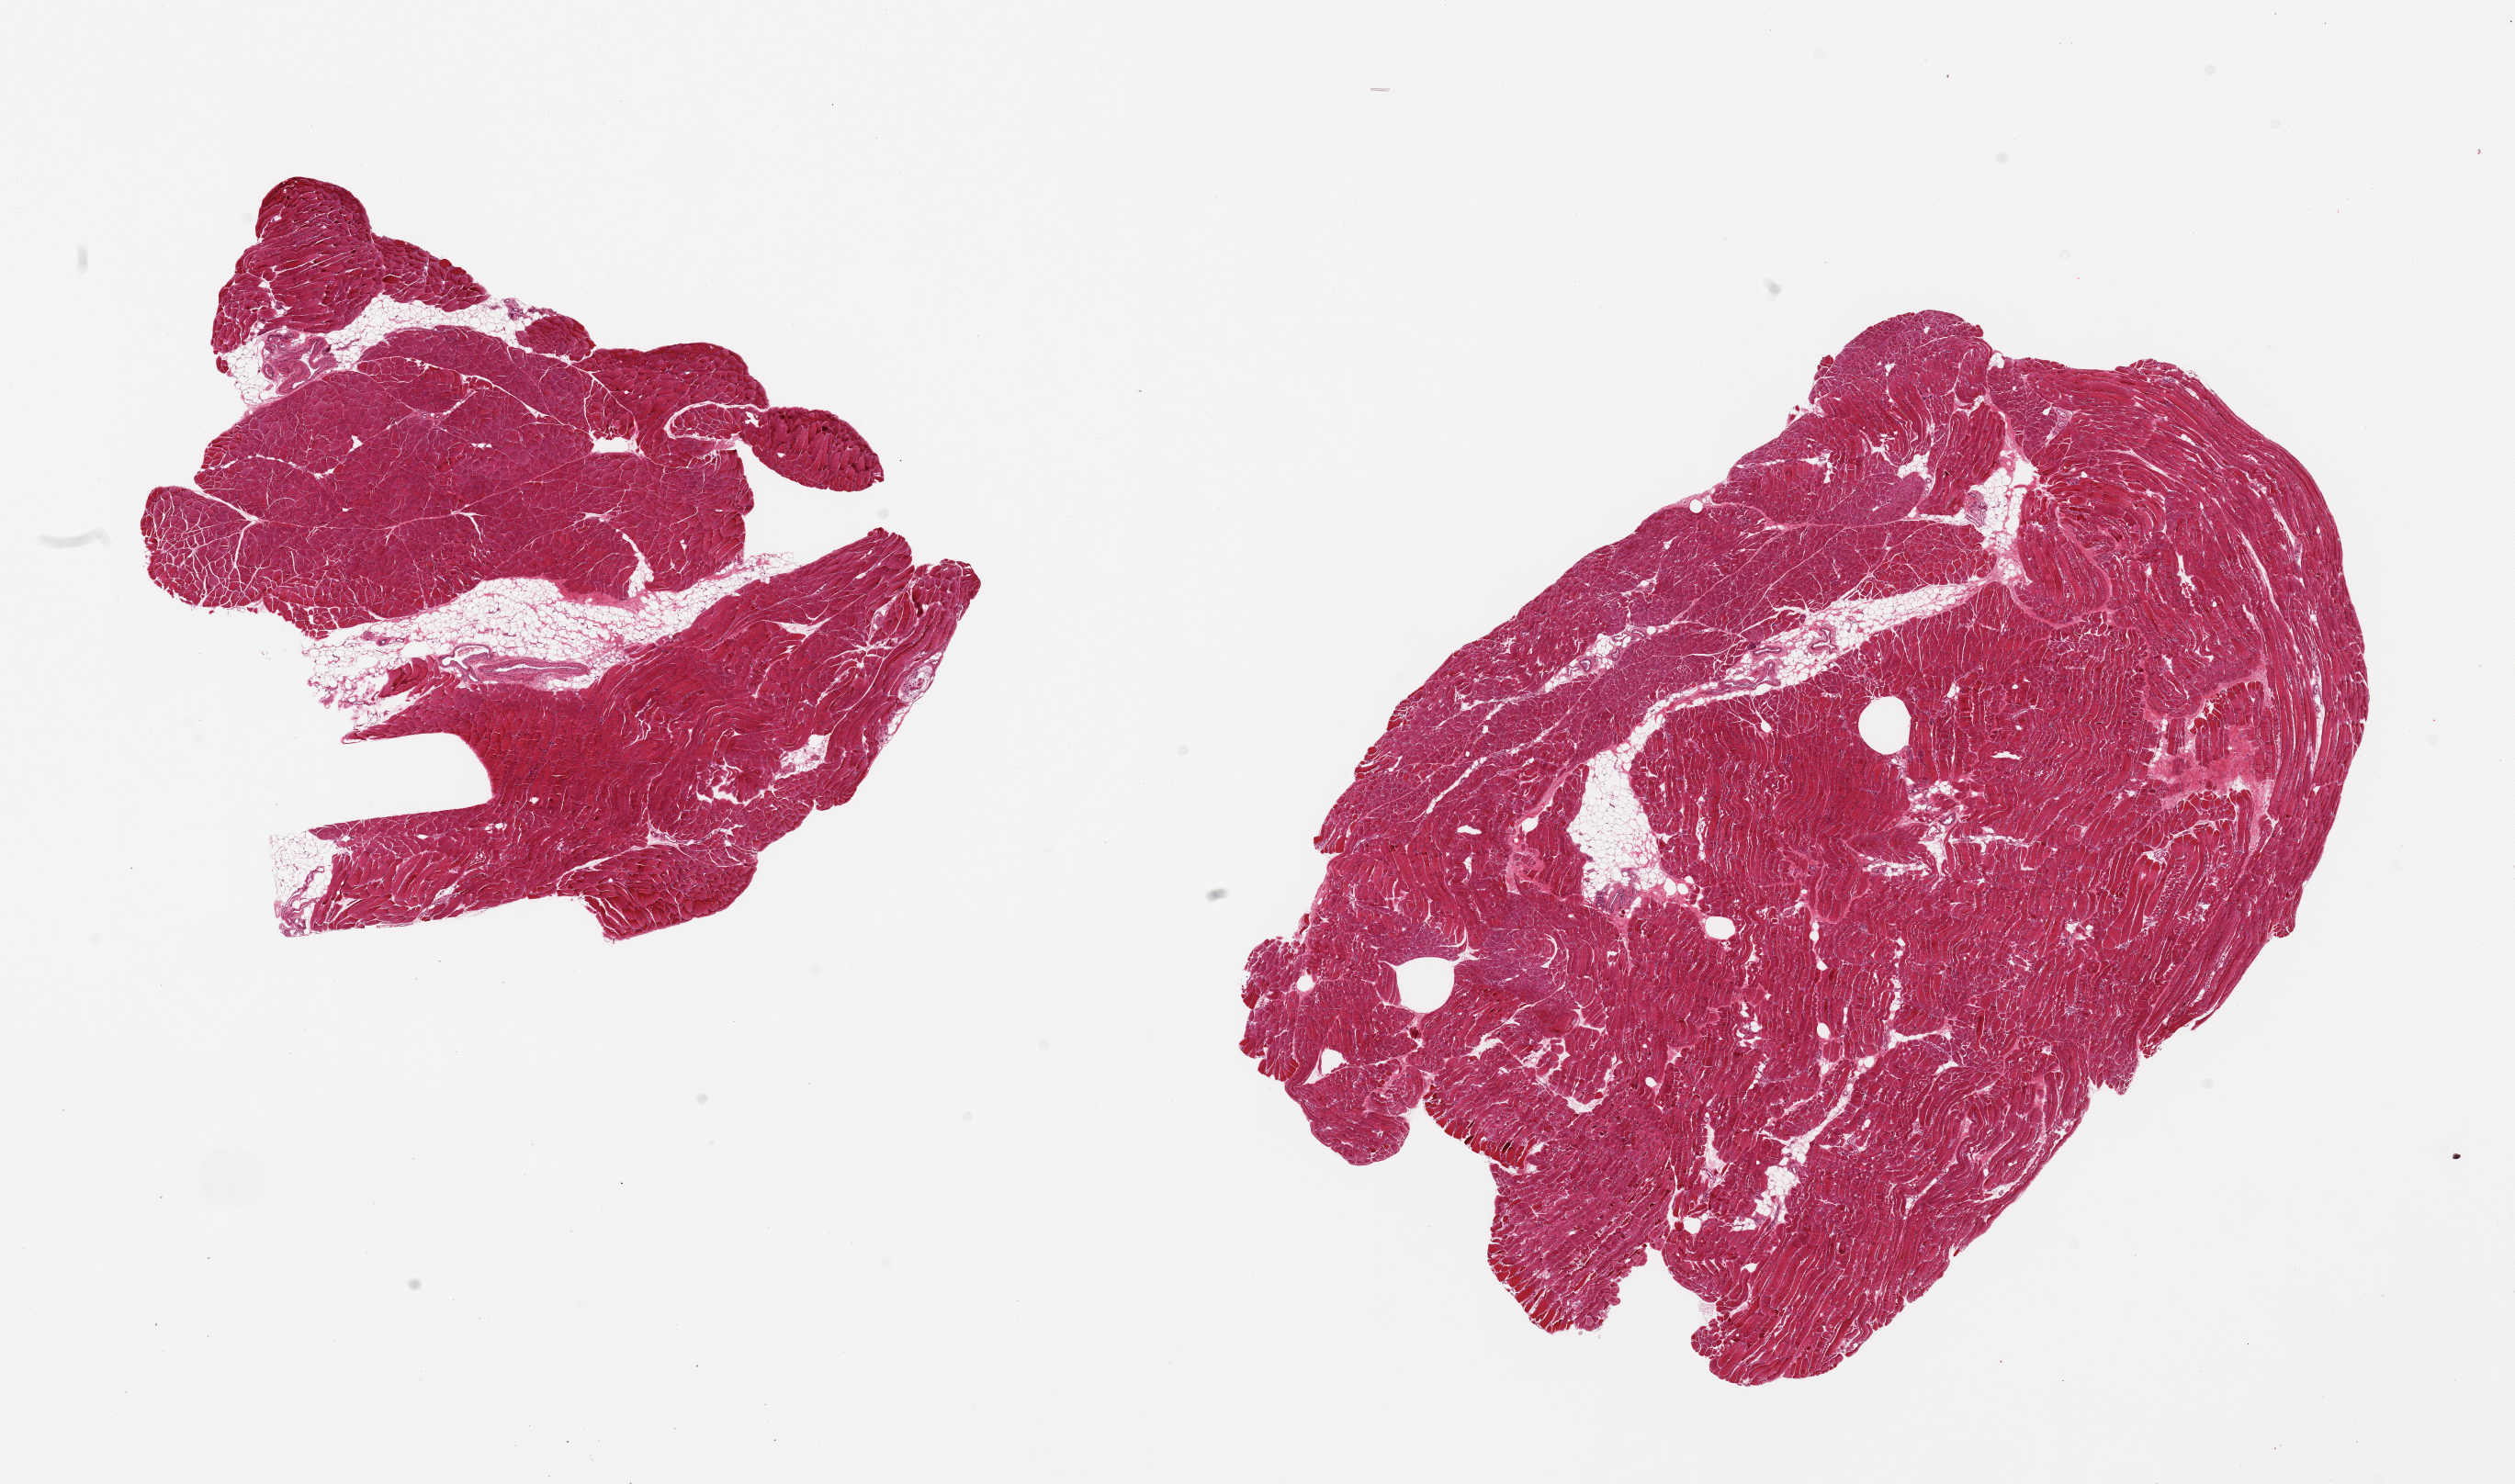
Hematoxylin and eosin (H&E) whole-slide image — low-resolution overview of the scanned area, about 21.7 x 12.8 mm; PAXgene-fixed paraffin-embedded (PFPE) section; sampled site (target tissue): skeletal muscle; tissue donor sample. Donor sex: female.
Review note (as recorded): 2 pieces, ~10% interstitial fat.